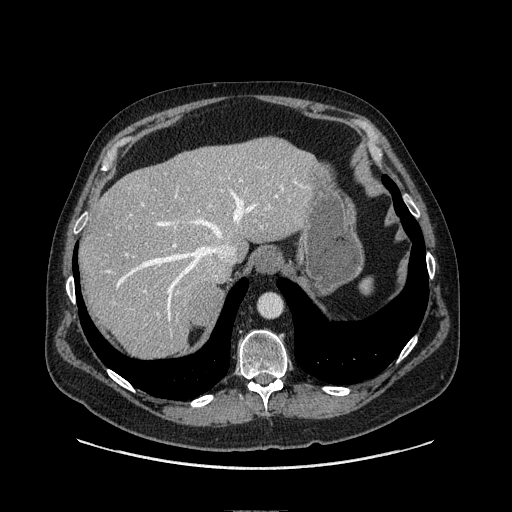
Contrast-enhanced abdominal CT, one axial slice. Slice 92 of 149 in the series (ordered by position). Soft-tissue window (W 400 / L 40 HU). 1.25 mm slice thickness. 512 × 512 image matrix, field of view 440 × 440 mm. Male patient. From the clinical record (not read from this slice): diagnosis: adrenocortical carcinoma; tumour side: right adrenal; tumour size at pathology: 7.5 cm; Ki-67 index: 15 %; stage (as recorded): 2.
Structures marked on this image (semi-automatically segmented with operator editing):
- mass: bounding box <193,287,219,326> (left, top, right, bottom; pixels)